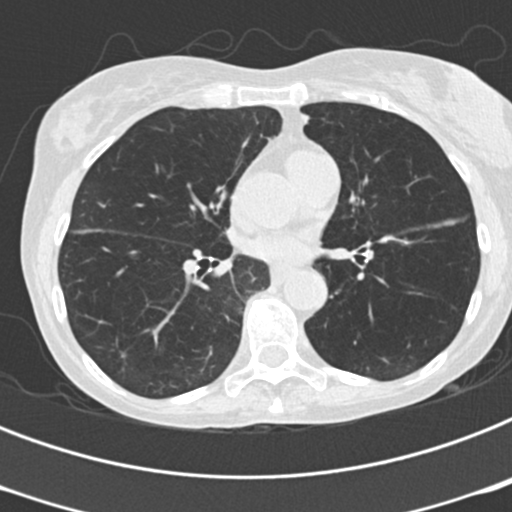
Low-dose screening chest CT, axial slice. Third screening round (two years after baseline). Lung window (W 1500 / L -600 HU). Slice 94 of 199 in the series. Female, age 68 years at enrolment. Former smoker at enrolment.
- Expert reader's lesion annotation, bounding box [x1, y1, x2, y2] px = [101, 338, 140, 370].
- Screening reader's record for this exam (one nodule recorded; not confirmed to be the boxed lesion): non-calcified nodule or mass ≥4 mm, right lower lobe, 9 × 5 mm, poorly defined margins, soft tissue attenuation, pre-existing on the prior screen: yes; interval growth: no.